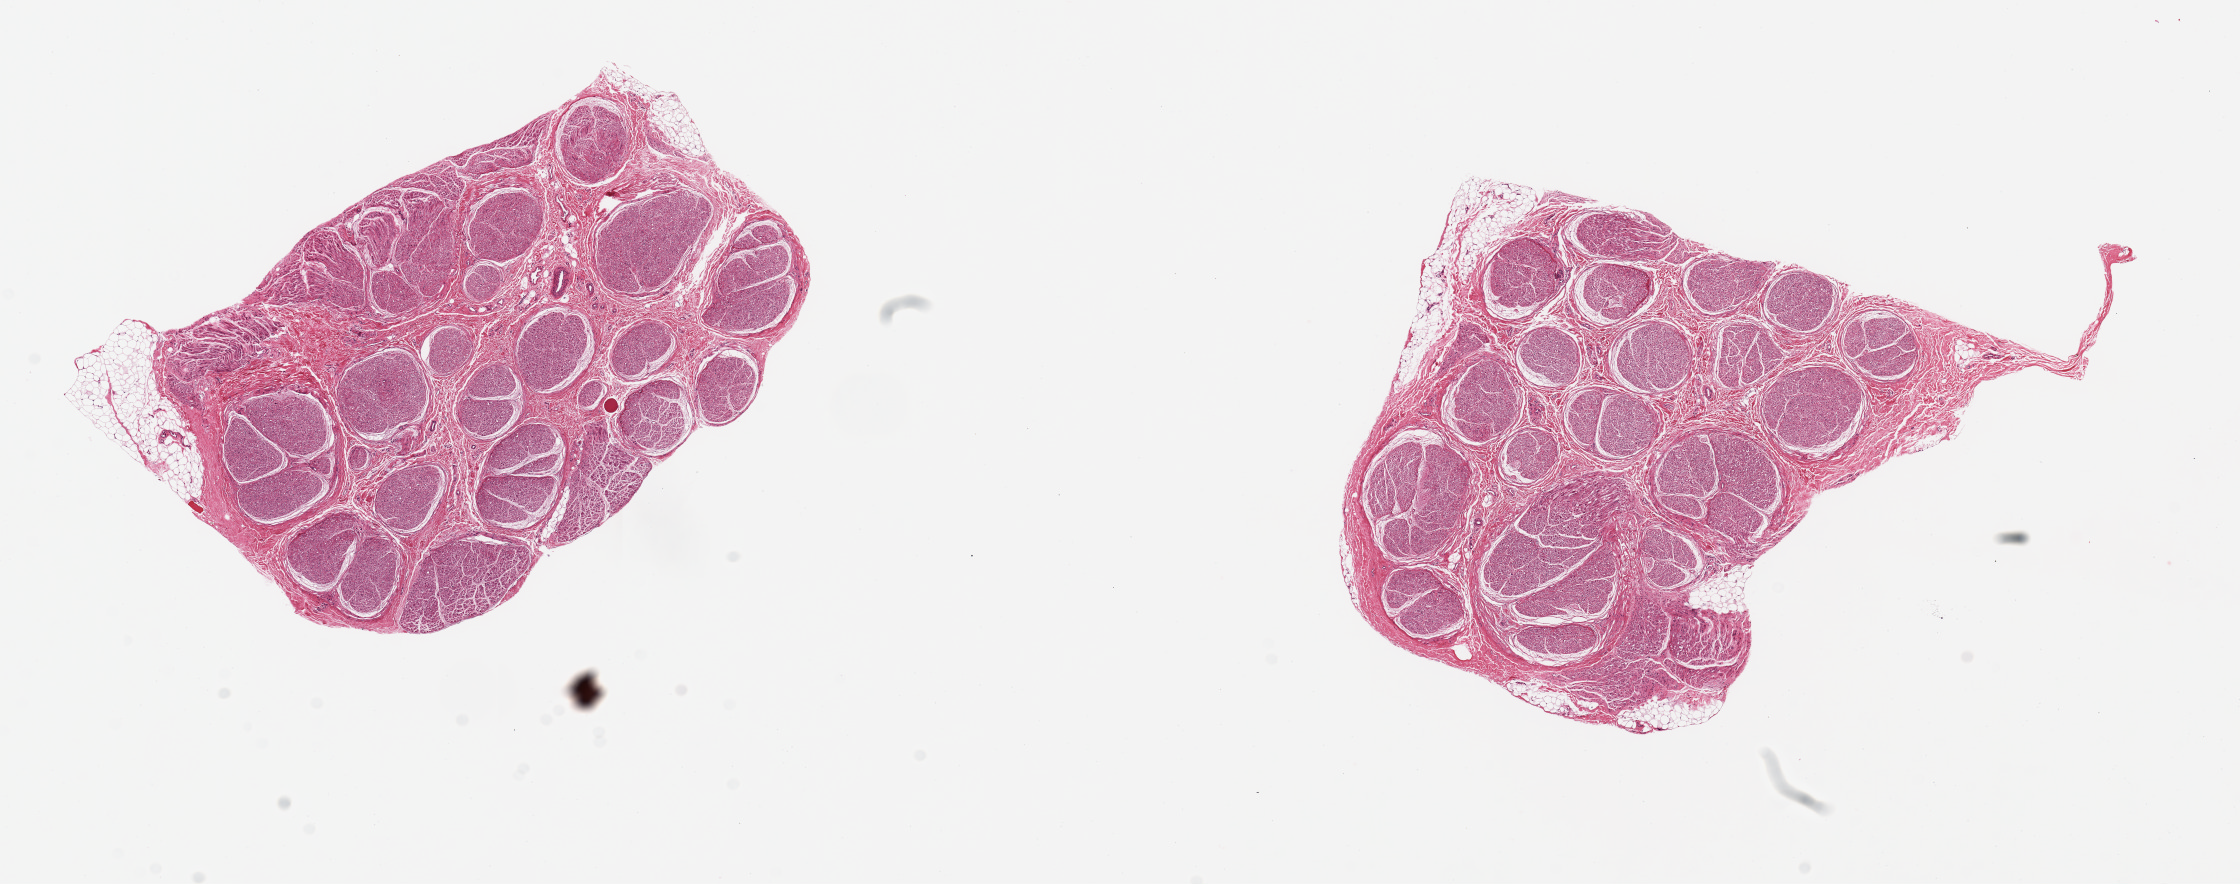
Whole-slide image, haematoxylin and eosin stain — shown as a low-resolution overview of the whole scanned area (about 17.7 x 7.0 mm, slide scanned at 20x). PAXgene-fixed paraffin-embedded (PFPE) section. Section of tibial nerve (target tissue). Donor tissue sample.
Pathologist's review note for this sample: 2 pieces 5x3 & 4x3 mm; <10% peripheral adipose.